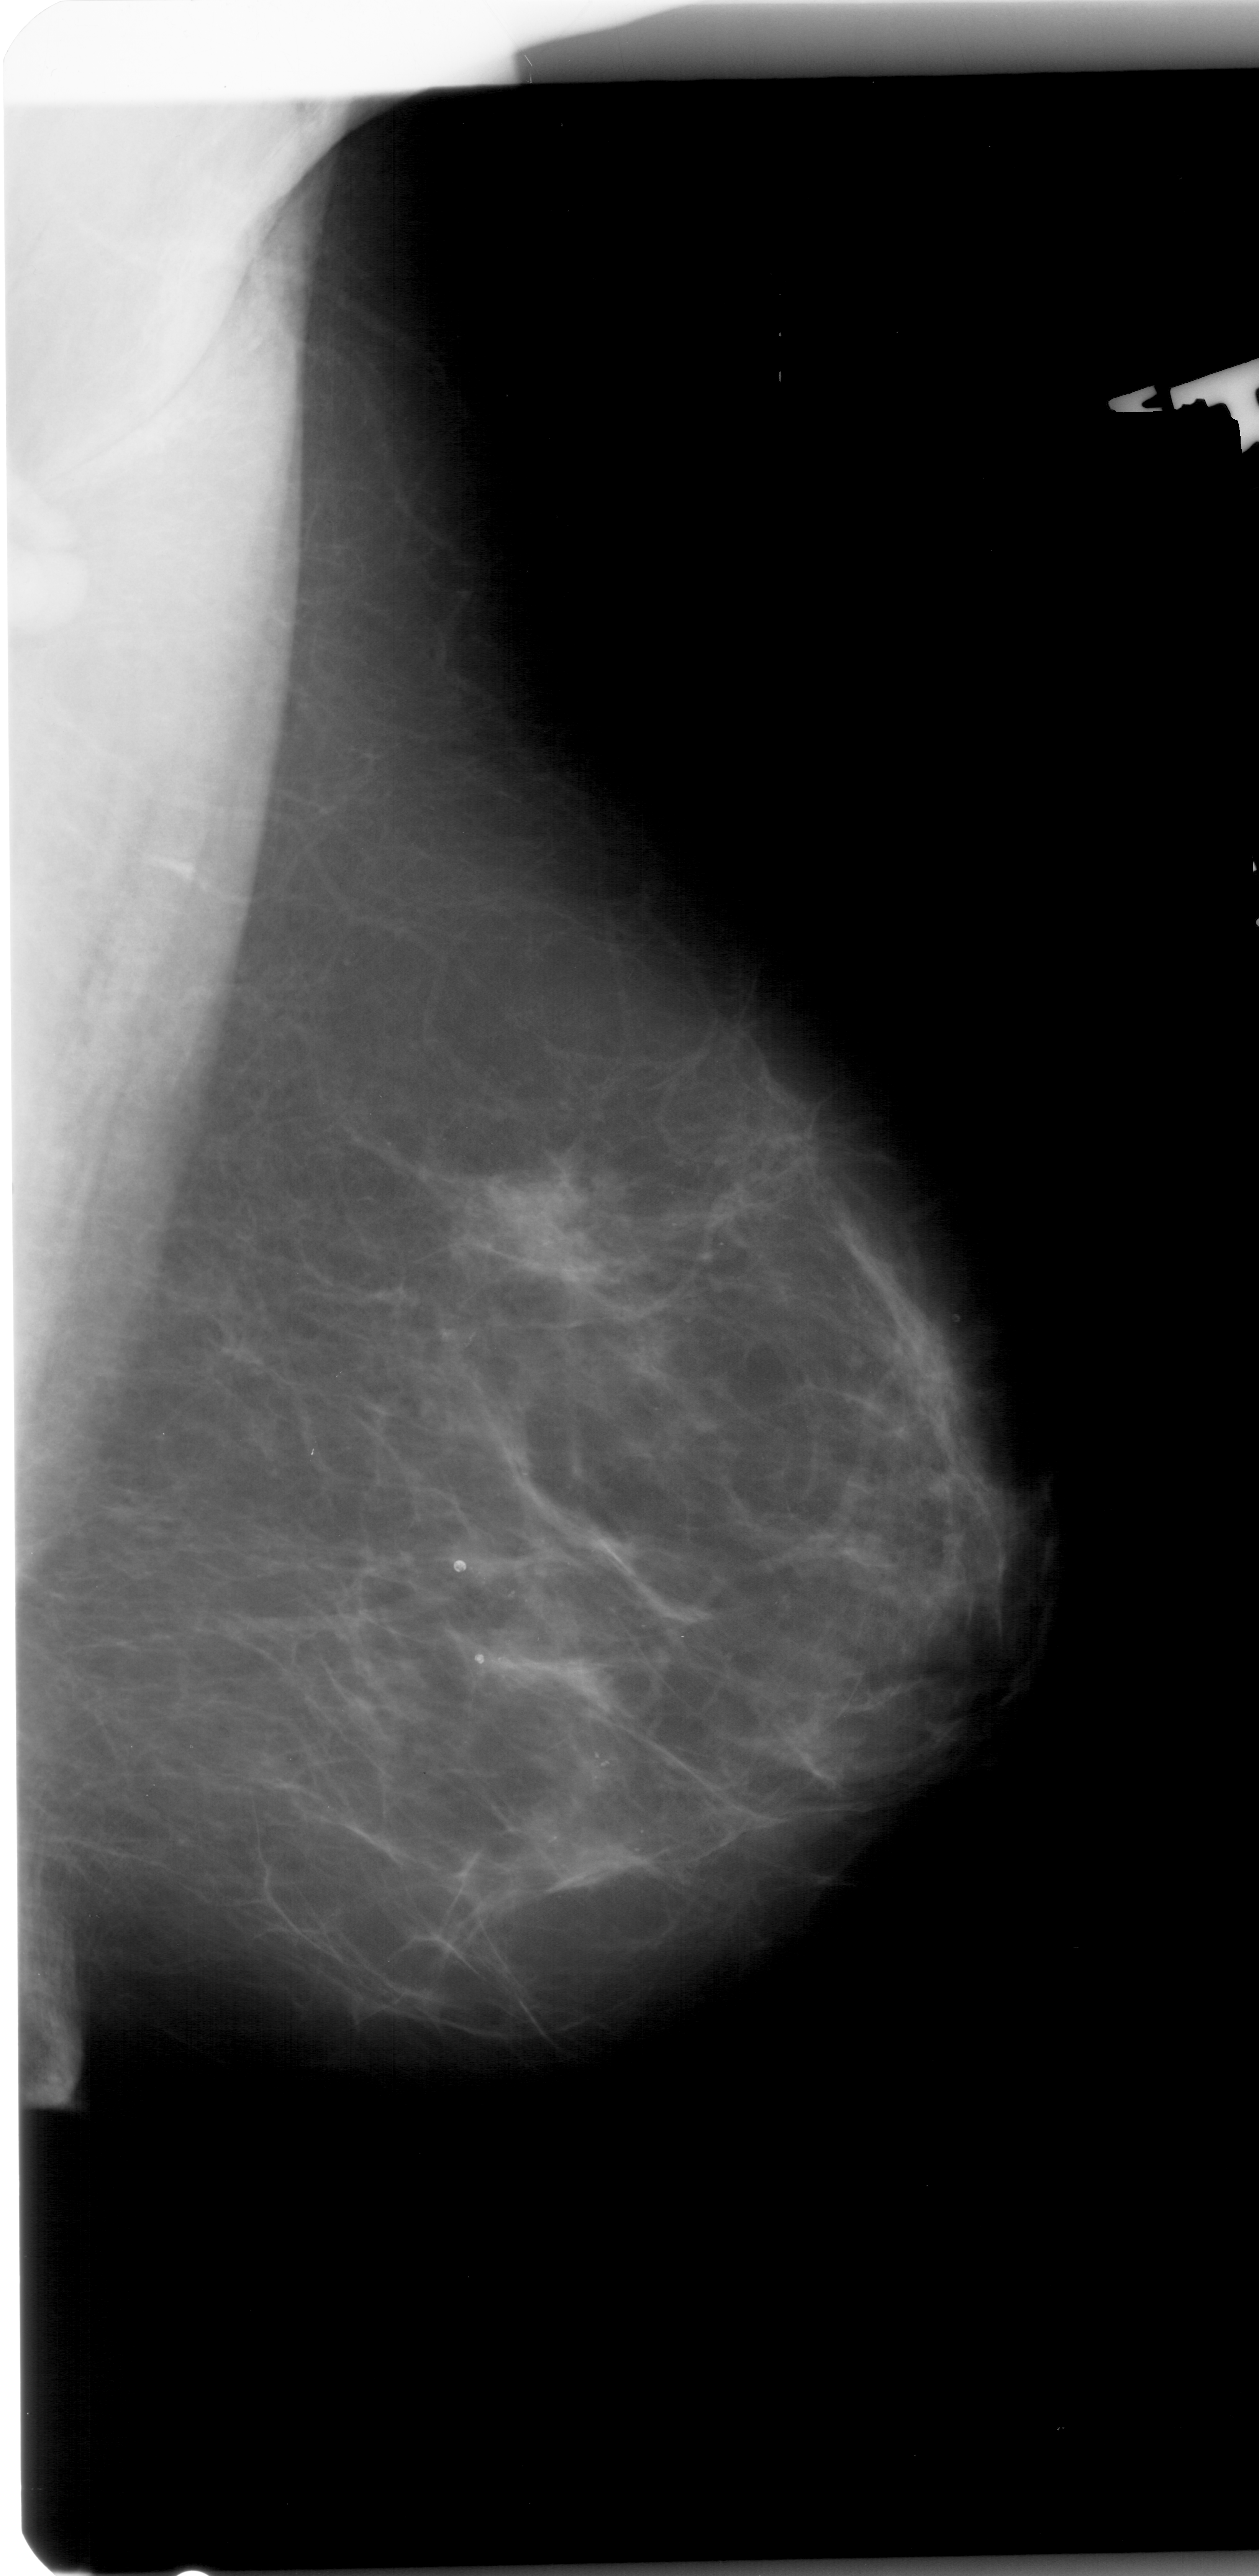
Mammogram (digitized film); right breast; mediolateral oblique (MLO) view; BI-RADS breast density category 2 (scale 1–4); 1259 × 2576 image matrix.
Expert-marked regions of interest on this film, with their recorded descriptors:
- calcifications, morphology pleomorphic, distribution clustered; BI-RADS assessment category 4; pathology (as recorded): benign: bounding box (x1, y1, x2, y2) in pixels: (452, 1320, 505, 1371)